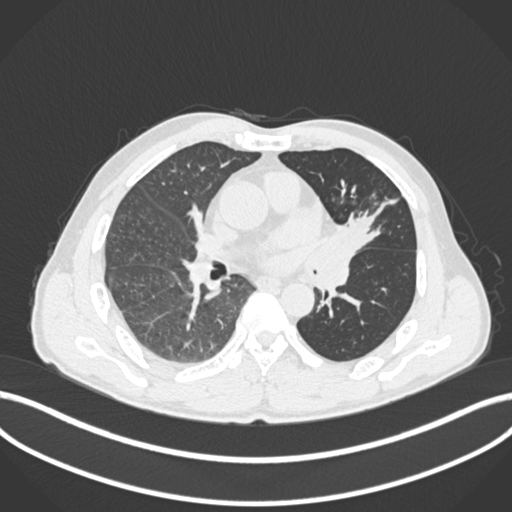
Chest CT, one axial slice; position 97 of 255 along the scan axis; lung window (W 1500 / L -600 HU); 1 mm slice thickness; 512 × 512 image matrix, field of view 400 × 400 mm. Male patient, age 57 years. From the clinical record (not read from this slice): clinical TNM (as recorded): T2b N0 M0.
Annotated regions visible in this slice (bounding box drawn by a radiologist):
- lung tumour (recorded histology: squamous cell carcinoma): bounding box [x1, y1, x2, y2] px = [313, 208, 381, 268]